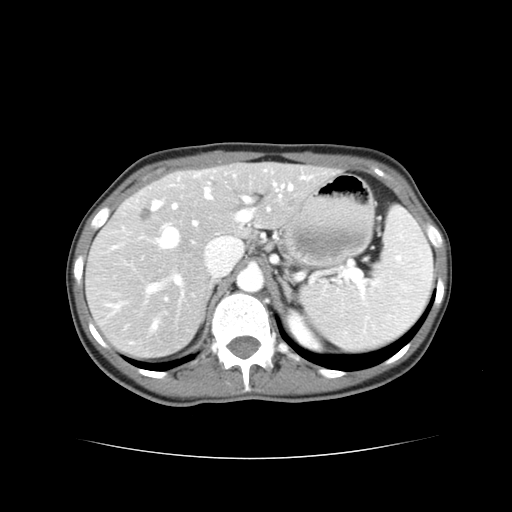
Contrast-enhanced abdominal CT, one axial slice. Position 26 of 38 along the scan axis. Reconstruction kernel STANDARD. Intravenous contrast given. Soft-tissue window (W 400 / L 40 HU). 5 mm slice thickness. 512 × 512 image matrix. Female patient, age 54 years. Case-level facts recorded for this patient, not image findings: diagnosis: colorectal cancer liver metastases, imaged before liver resection; multiple liver metastases: yes; largest metastasis: 1.1 cm.
Outlined on this slice (expert manual segmentation):
- hepatic veins: box from (x=160, y=186) to (x=293, y=248) px
- liver: (x=87, y=164)–(x=332, y=359)
- planned liver remnant (the part of the liver to remain after resection): (x=212, y=164)–(x=333, y=235)
- portal vein (with intrahepatic branches): (x=149, y=177)–(x=306, y=292)
- liver metastasis: (x=141, y=209)–(x=151, y=221)